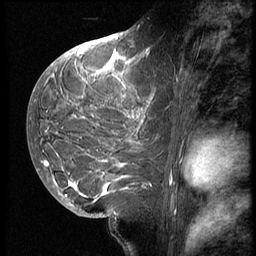
Breast MRI (dynamic contrast-enhanced), one sagittal slice. Position 27 of 62 along the scan axis. 3 images stored at this slice position (order not interpretable as contrast timing). 1.5 T. TE 4.2 ms, TR 9 ms. 2.5 mm slice thickness. 256 × 256 image matrix, field of view 180 × 180 mm. Patient: female, 28 years. Case-level facts recorded for this patient, not image findings: setting: breast cancer imaged before/during neoadjuvant chemotherapy.
Structures marked on this image (semi-automatic segmentation, software-assisted and operator-edited):
- analysis volume of interest (the breast-tissue region the enhancement analysis was run in; not a lesion): bounding box (x1, y1, x2, y2) in pixels: (42, 45, 164, 207)
- tumour enhancement mask (voxels above the 140 % enhancement threshold inside the analysis volume of interest): (42, 48, 151, 198)